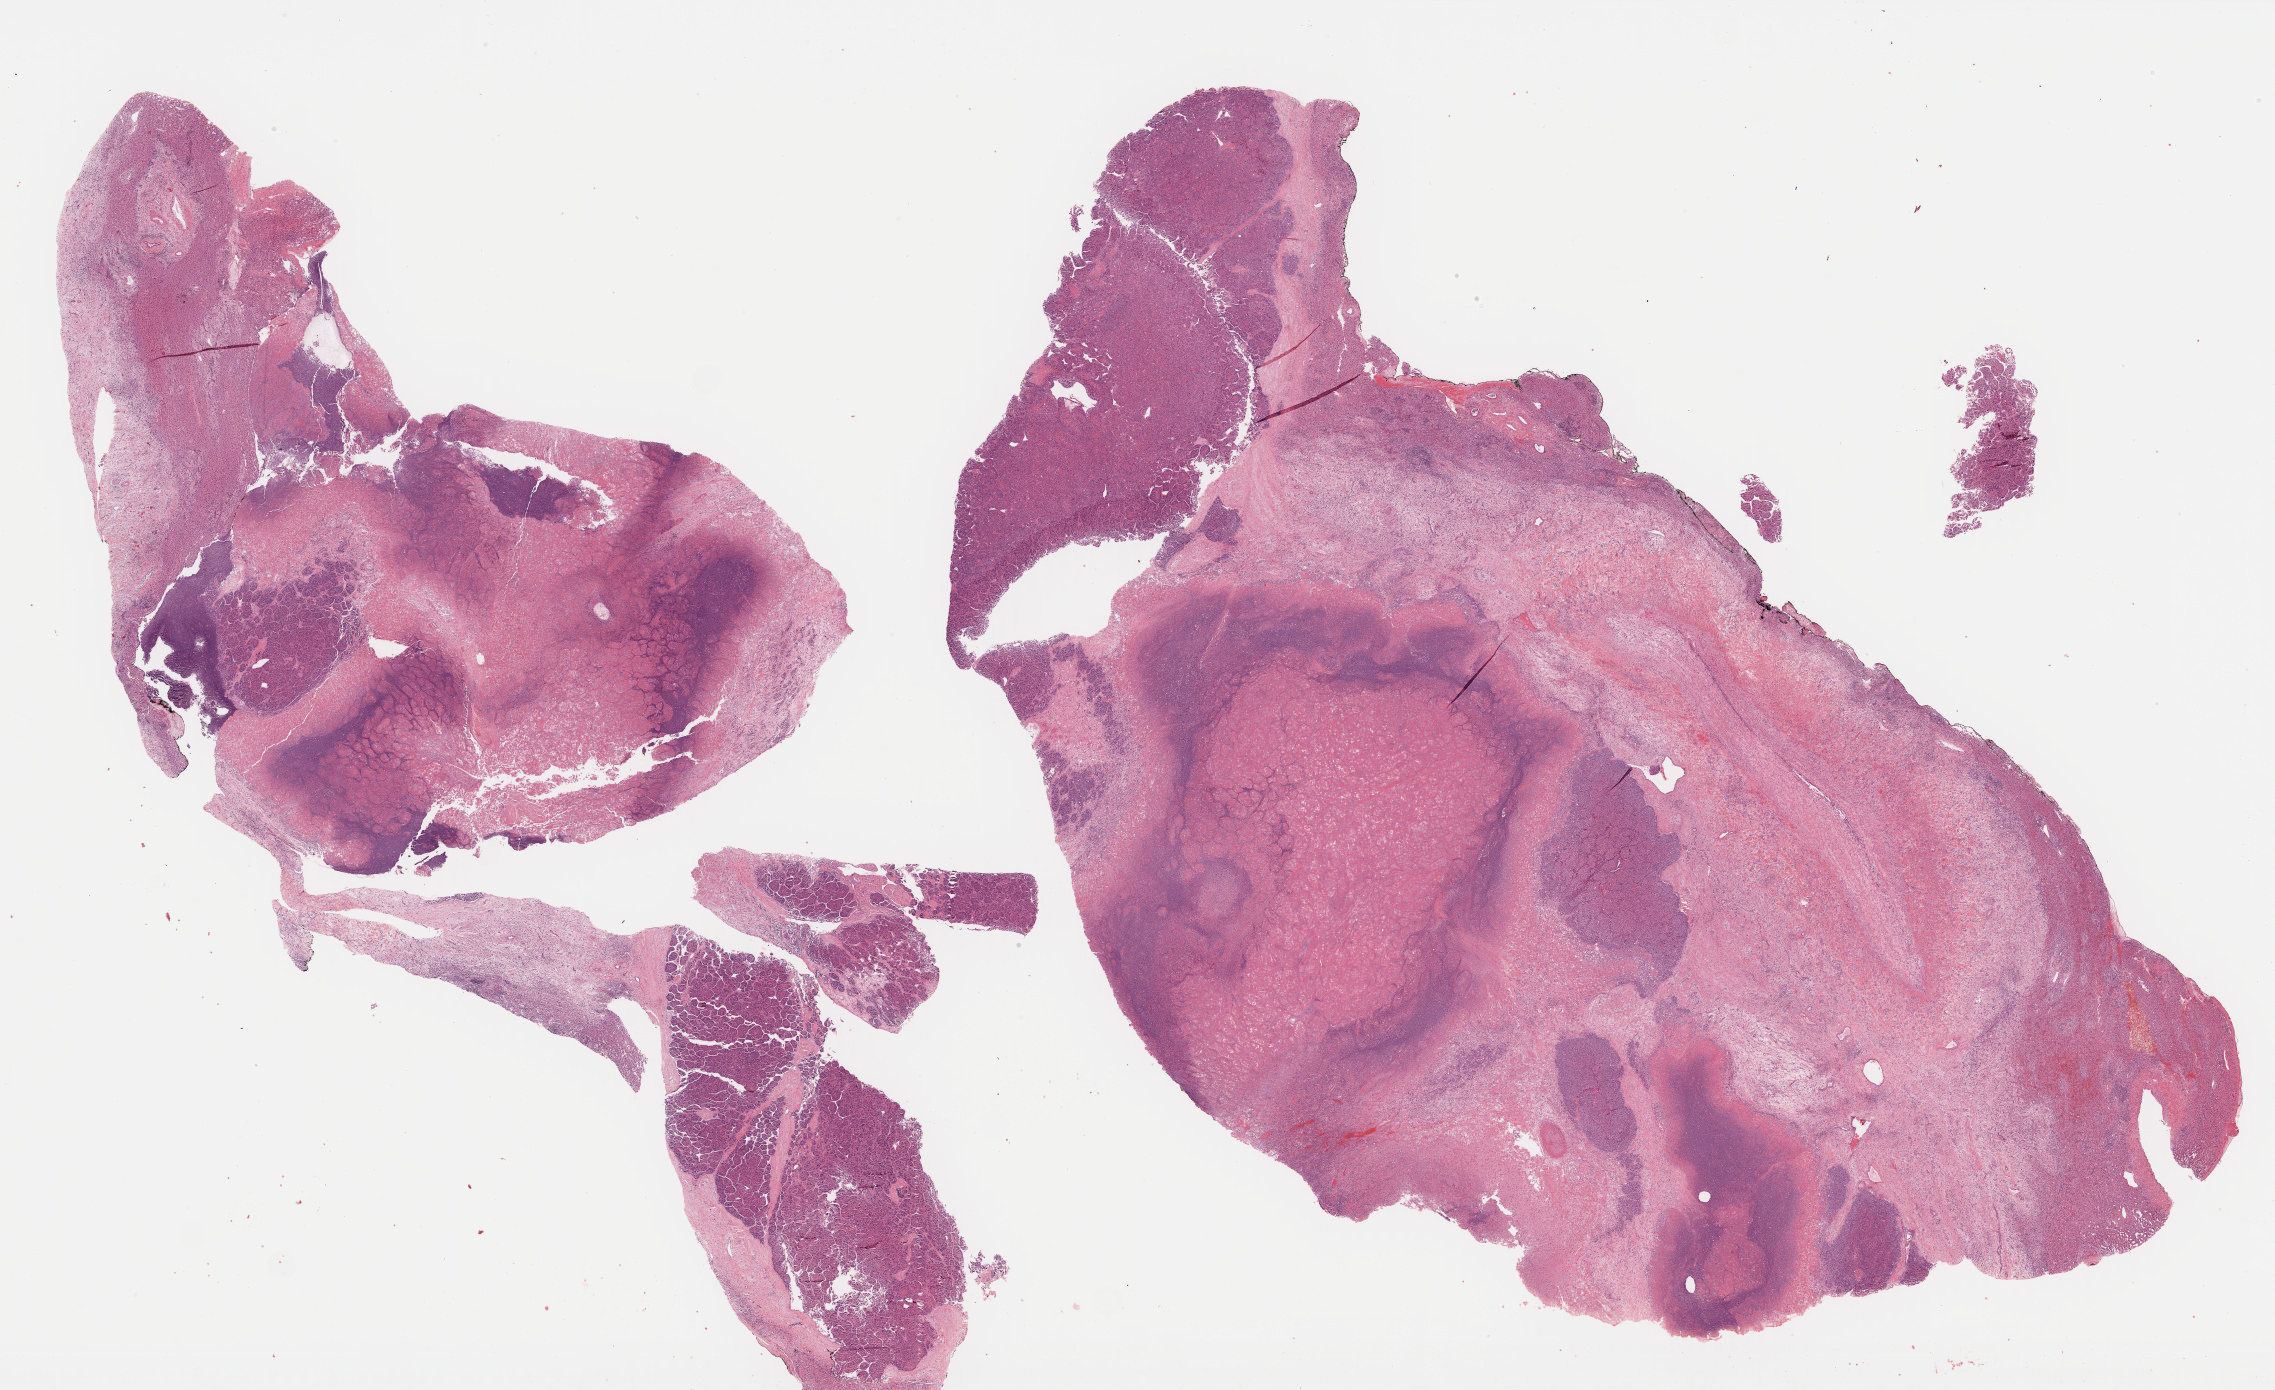
Hematoxylin and eosin (H&E) stained whole-slide image — a low-resolution overview of the entire scanned area, about 36.8 x 22.5 mm. Formalin-fixed paraffin-embedded (FFPE) diagnostic section. Sample: primary tumour, liver. Female patient; age at initial diagnosis 73 years.
Histologic diagnosis: Hepatocellular carcinoma, NOS.